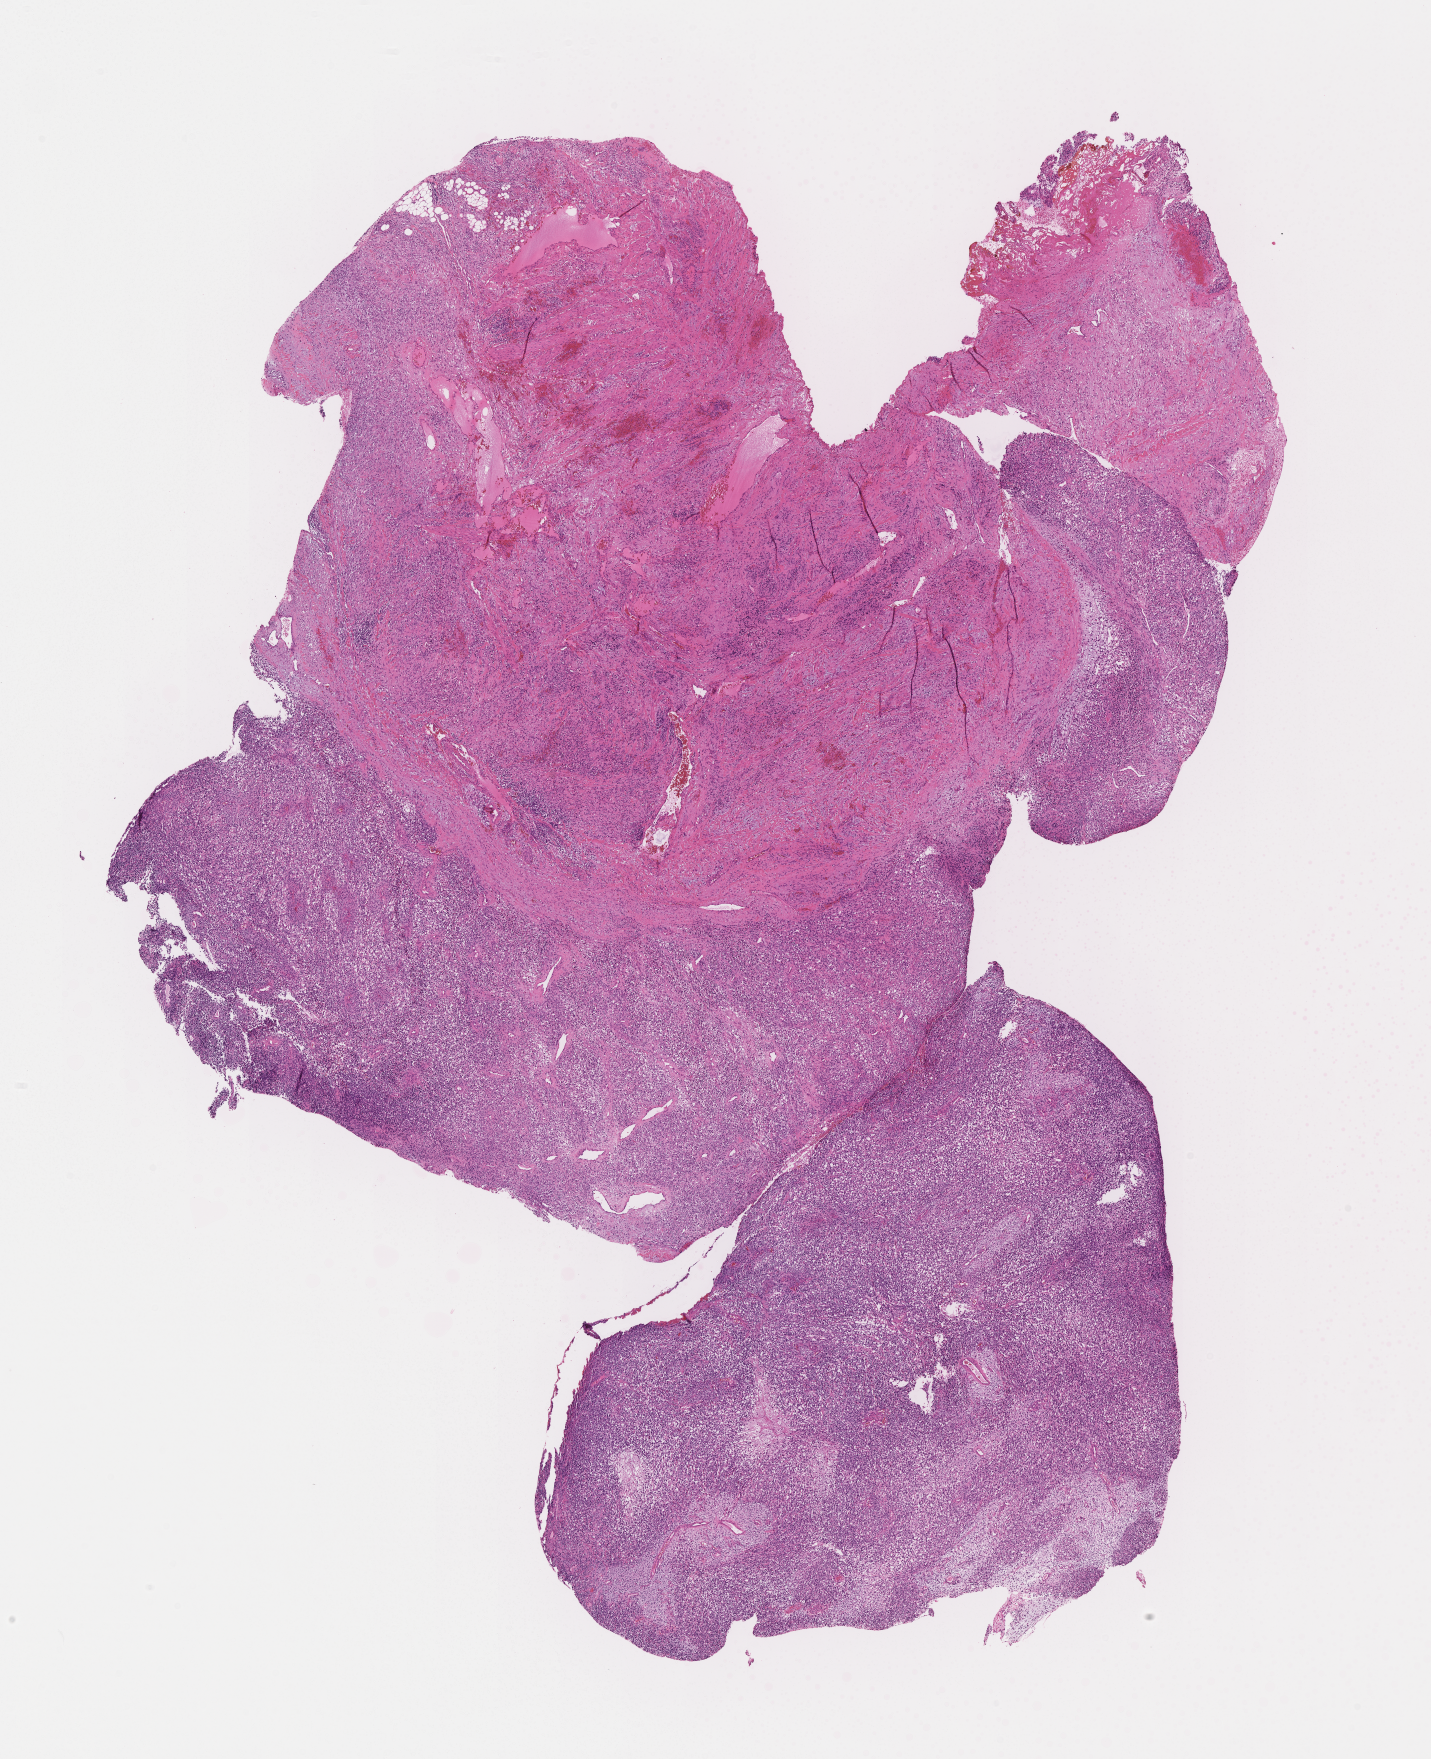
Whole-slide image, haematoxylin and eosin stain of tumor tissue — shown as a low-resolution overview of the whole scanned area (about 11.6 x 14.2 mm), formalin-fixed, paraffin-embedded (FFPE) tissue, site: pelvis. Female patient, age at diagnosis 11.8 years.
- metastatic status at presentation (as recorded): non-metastatic
- stage (as recorded): 3
- diagnosis: rhabdomyosarcoma; histological classification: embryonal rhabdomyosarcoma